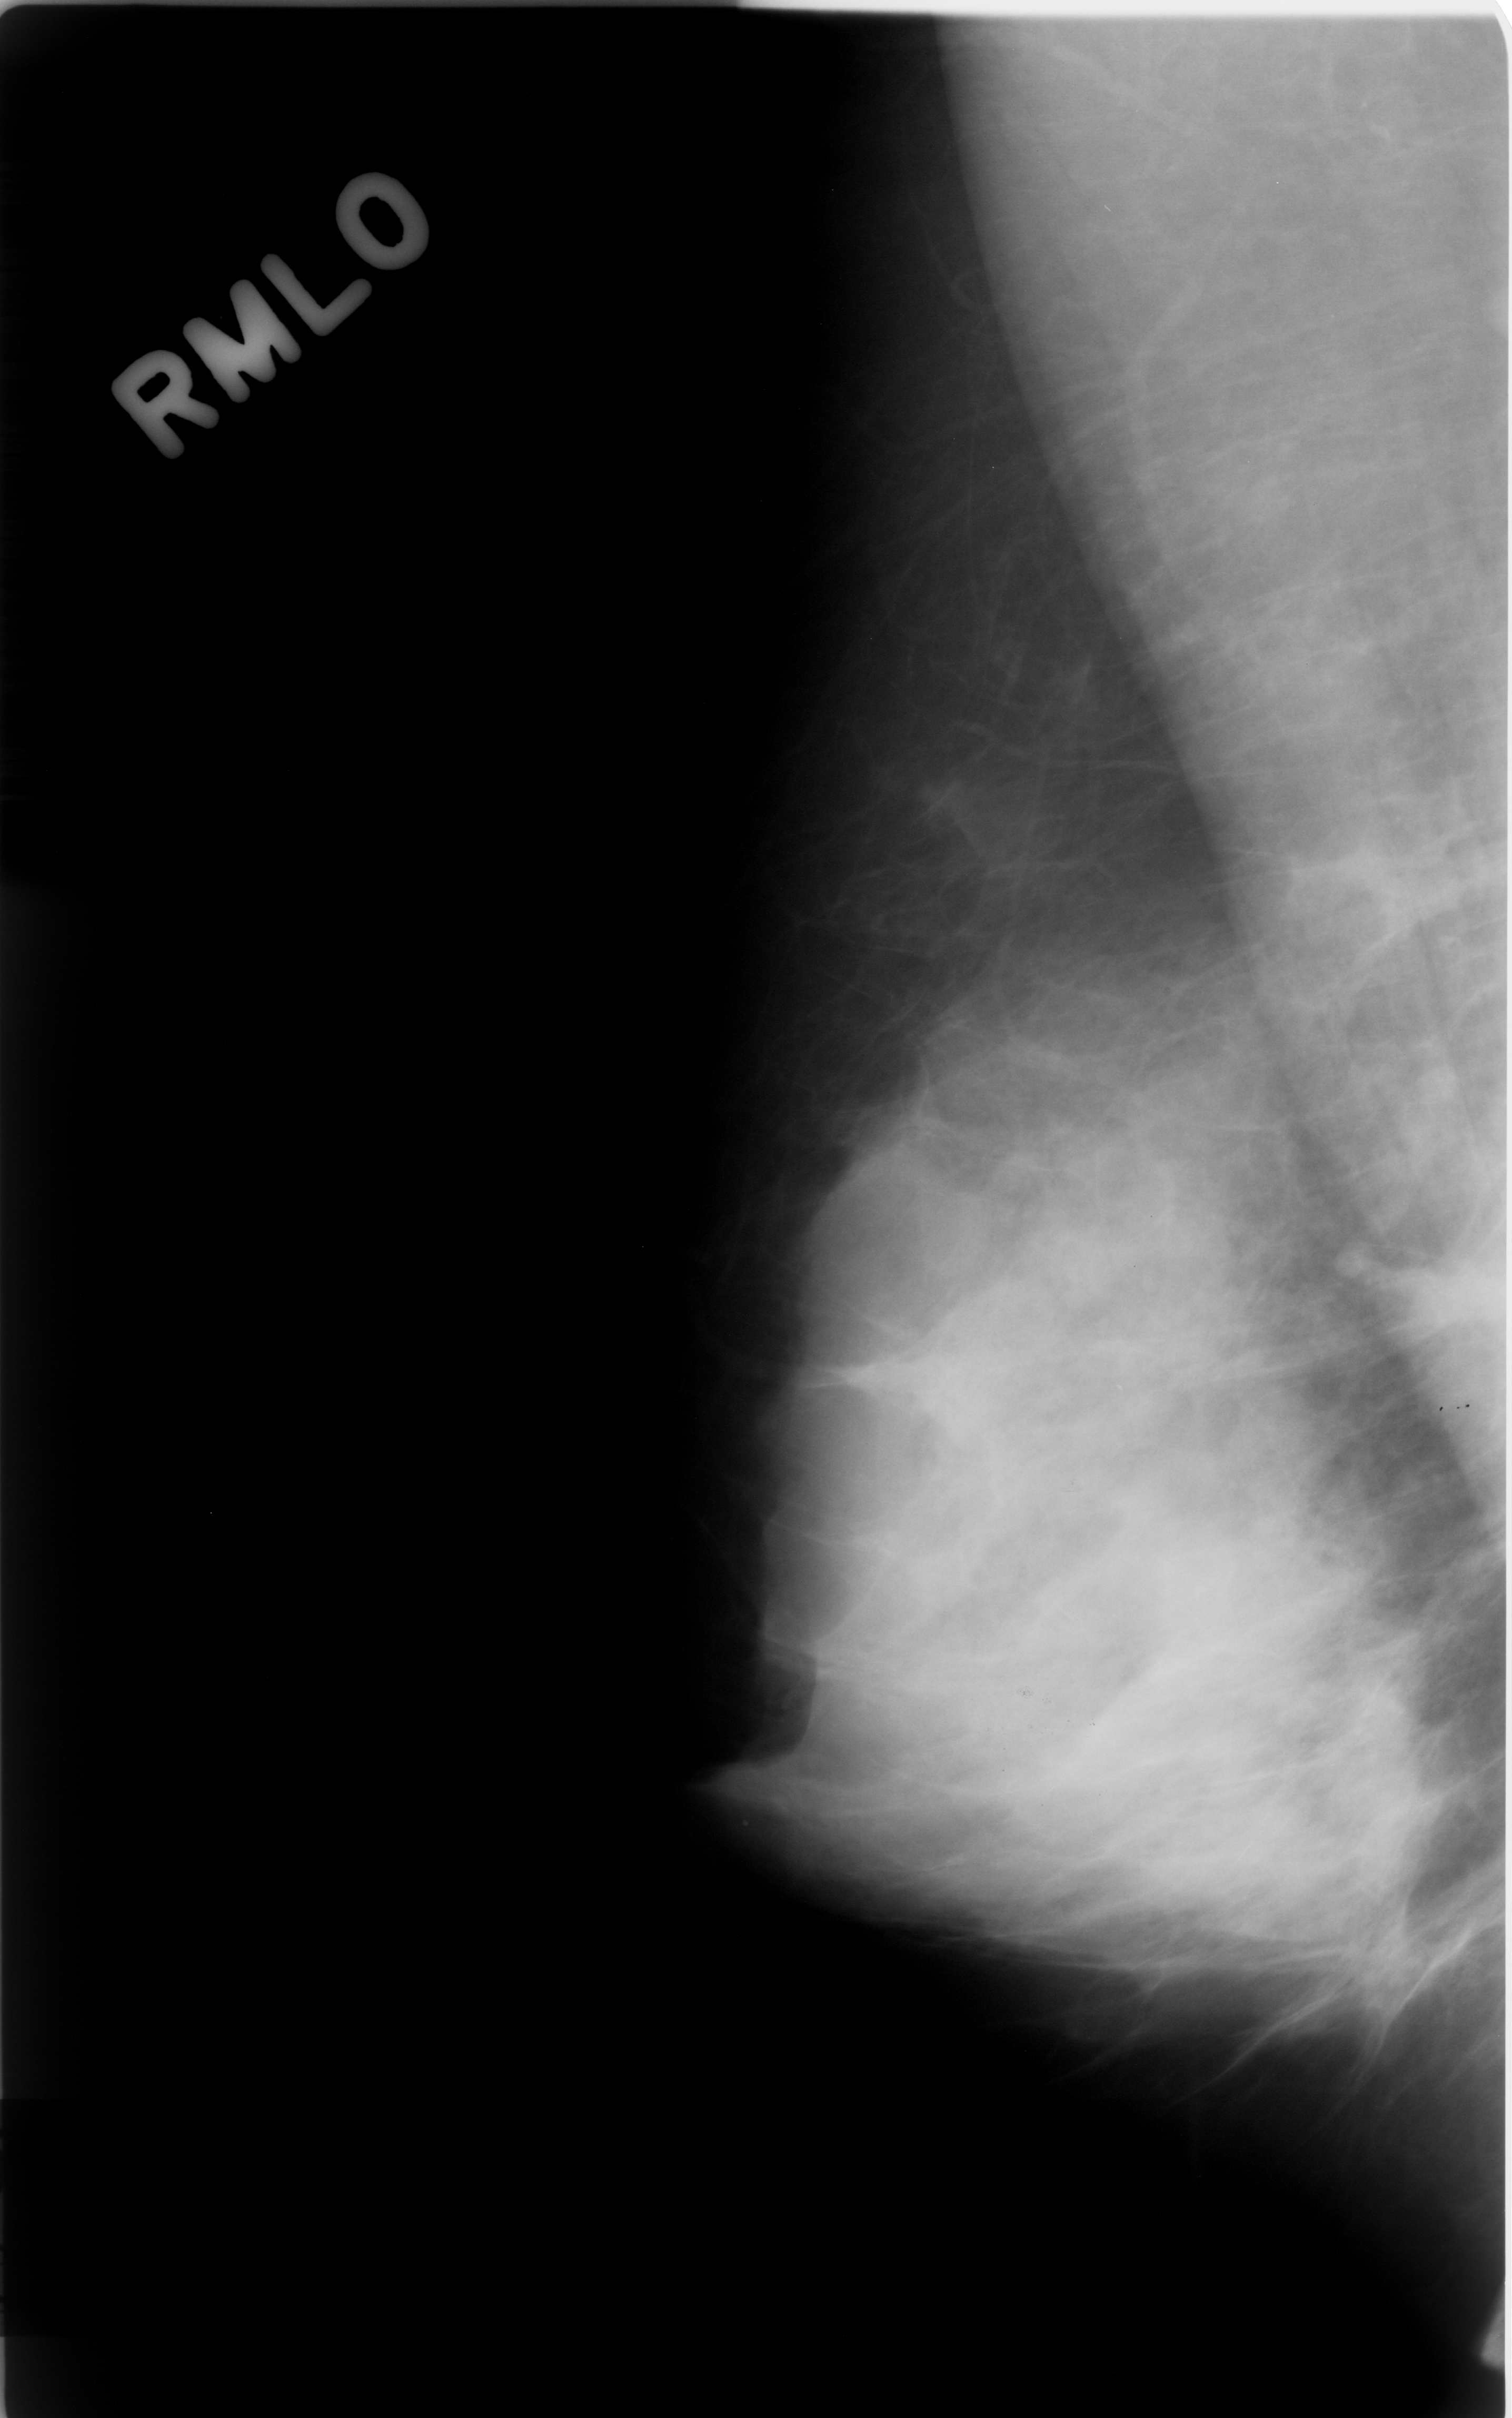
Mammogram (digitized film). Right breast. MLO view. Breast composition: extremely dense (BI-RADS density category 4 of 4). 1512 × 2418 image matrix.
Marked abnormalities (boxes around the expert regions of interest):
- mass, shape irregular, margins spiculated; BI-RADS assessment category 4; benign; no additional work-up was recommended (outcome (as recorded, no biopsy): benign without callback): bounding box [x1, y1, x2, y2] px = [1335, 1199, 1512, 1439]